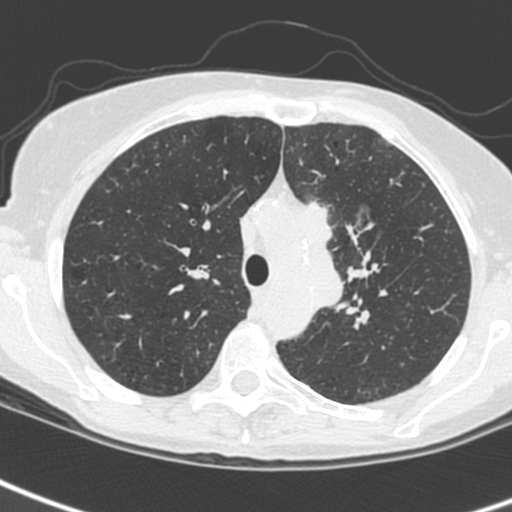
Low-dose screening chest CT, one axial slice; slice 183 of 242 in the series (ordered by position); 120 kVp; lung window (W 1500 / L -600 HU); 1.3 mm slice thickness; 512 × 512 image matrix.
Annotated regions visible in this slice (expert manual segmentation):
- lesion 3 (tumor, upper lobe of left lung): bounding box (x1, y1, x2, y2) in pixels: (298, 200, 343, 308)